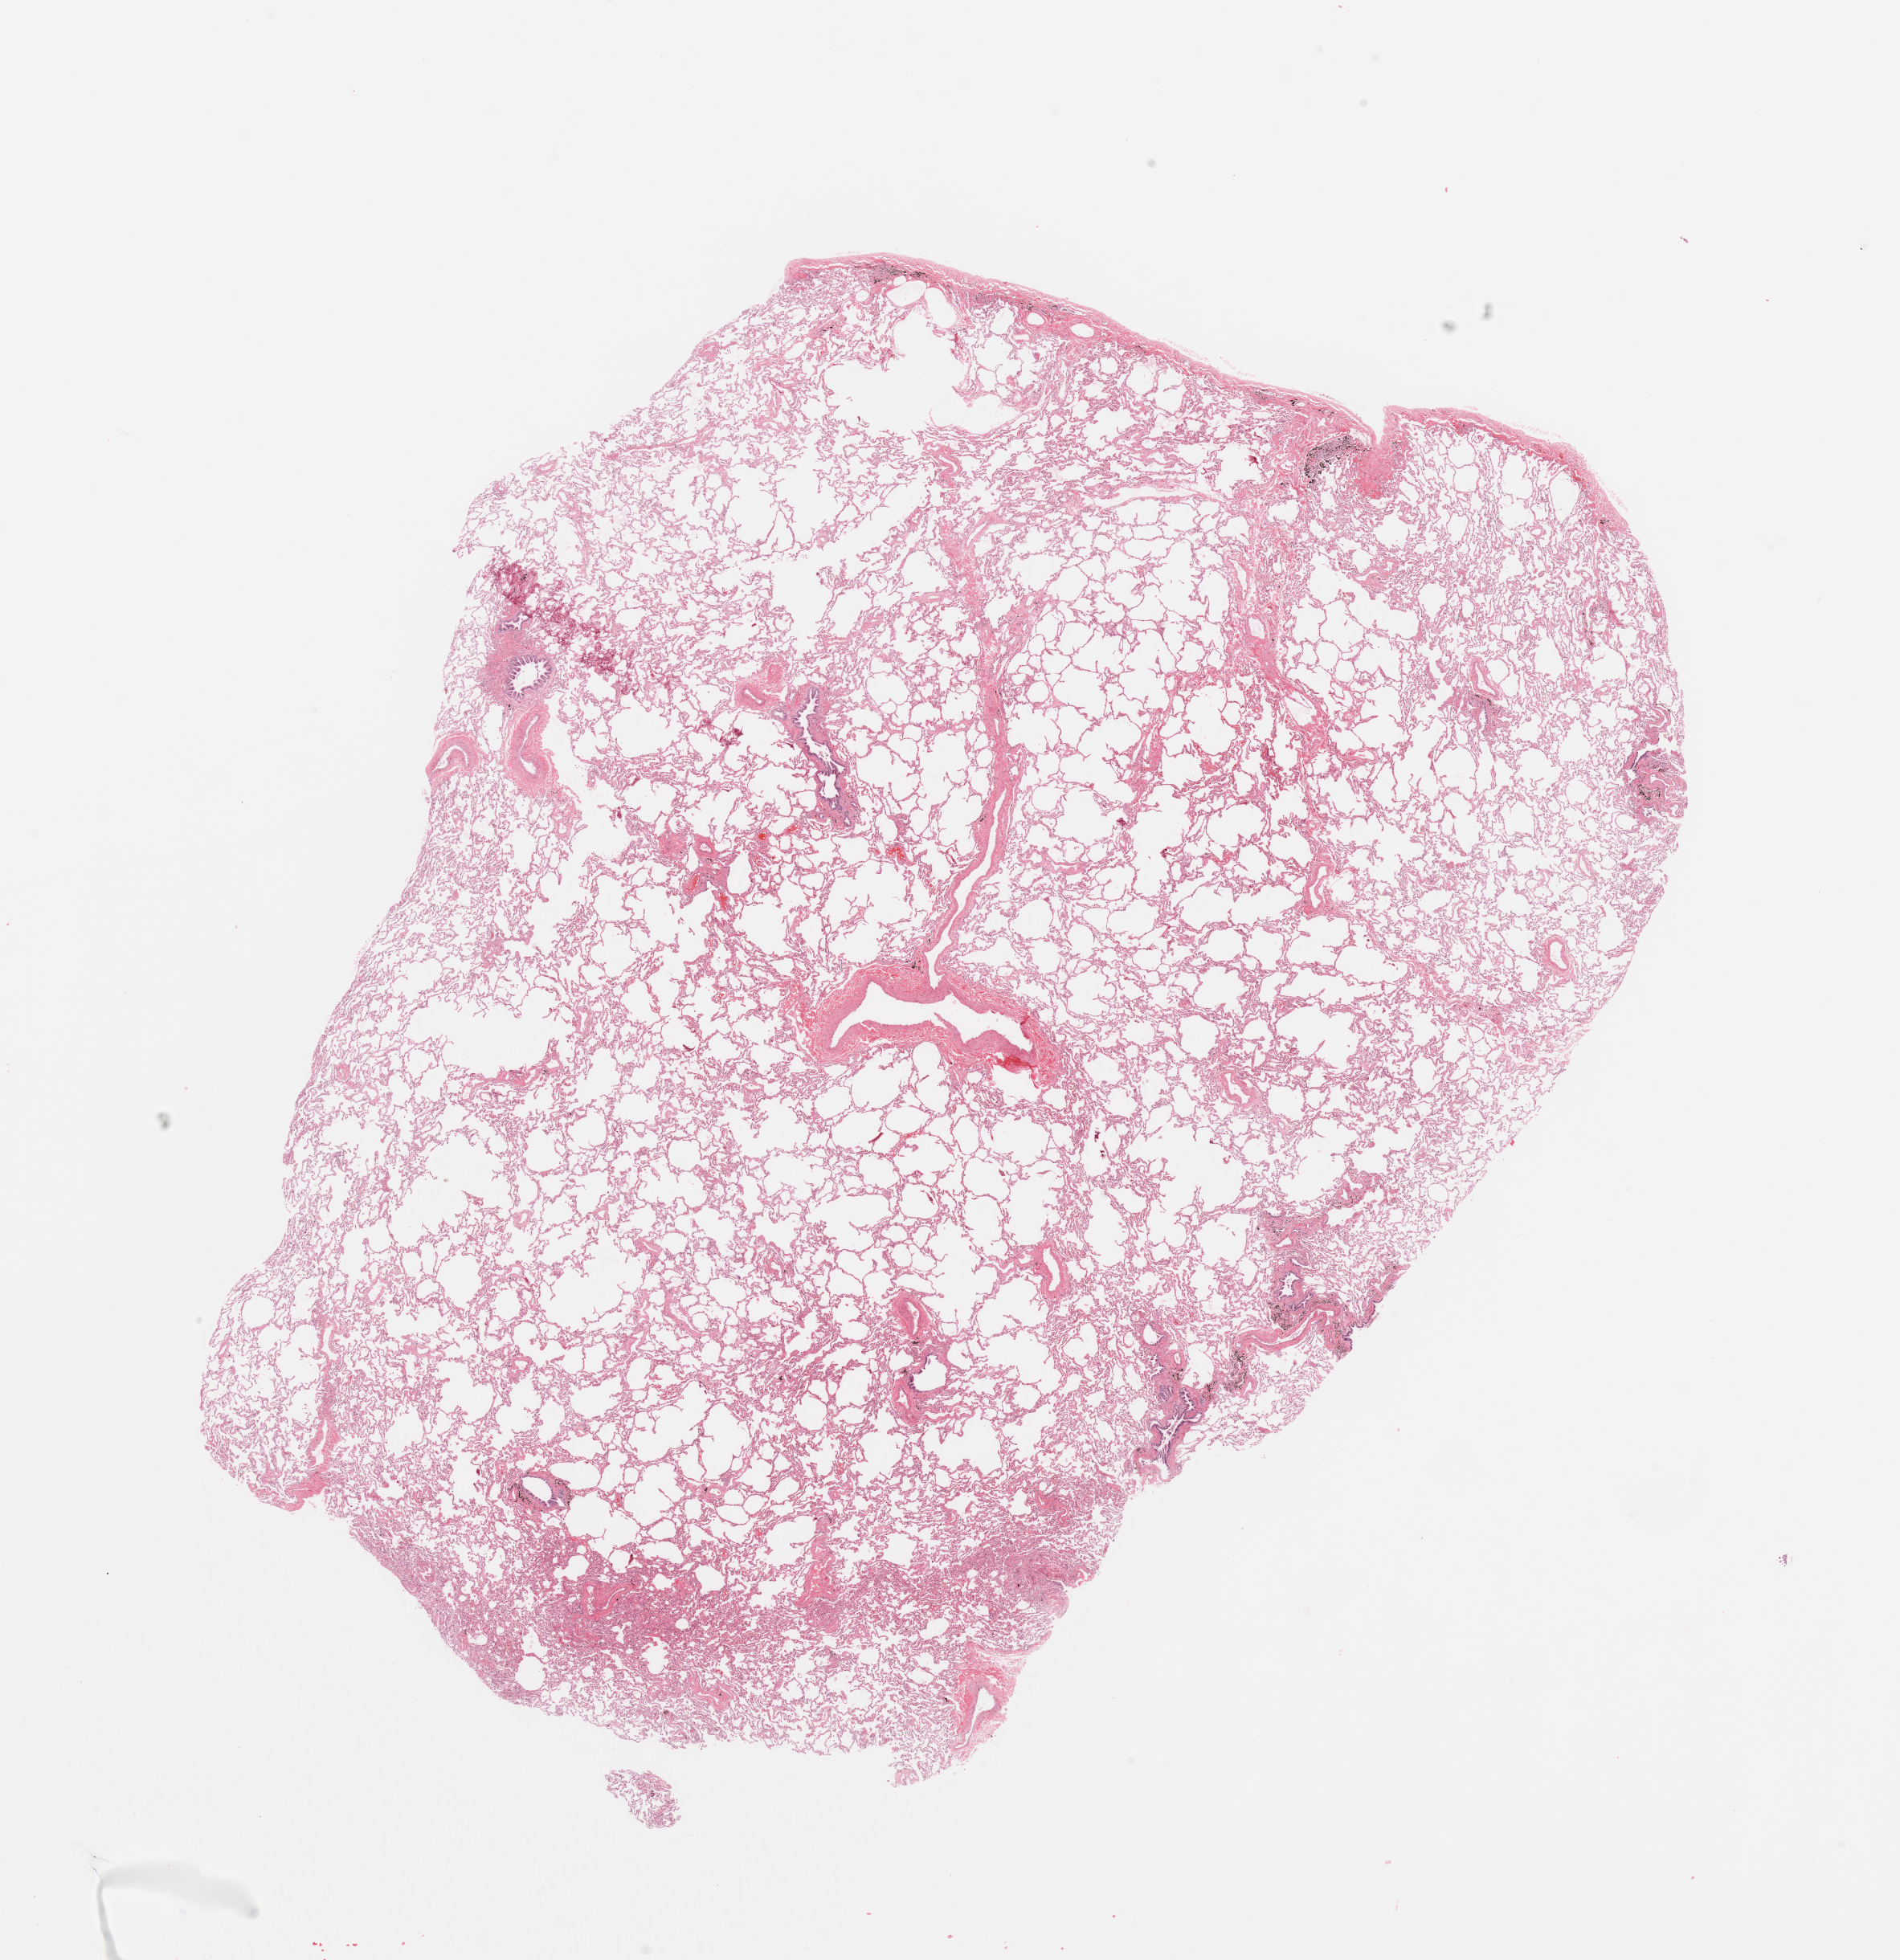
H&E whole-slide image — low-resolution overview of the scanned area, about 18.7 x 19.3 mm (acquisition: 20x scan). Lung, normal (non-tumour) tissue. Female, 49 y/o.
* this section: normal (non-tumour) tissue from the same patient
* patient diagnosis: Adenocarcinoma, NOS